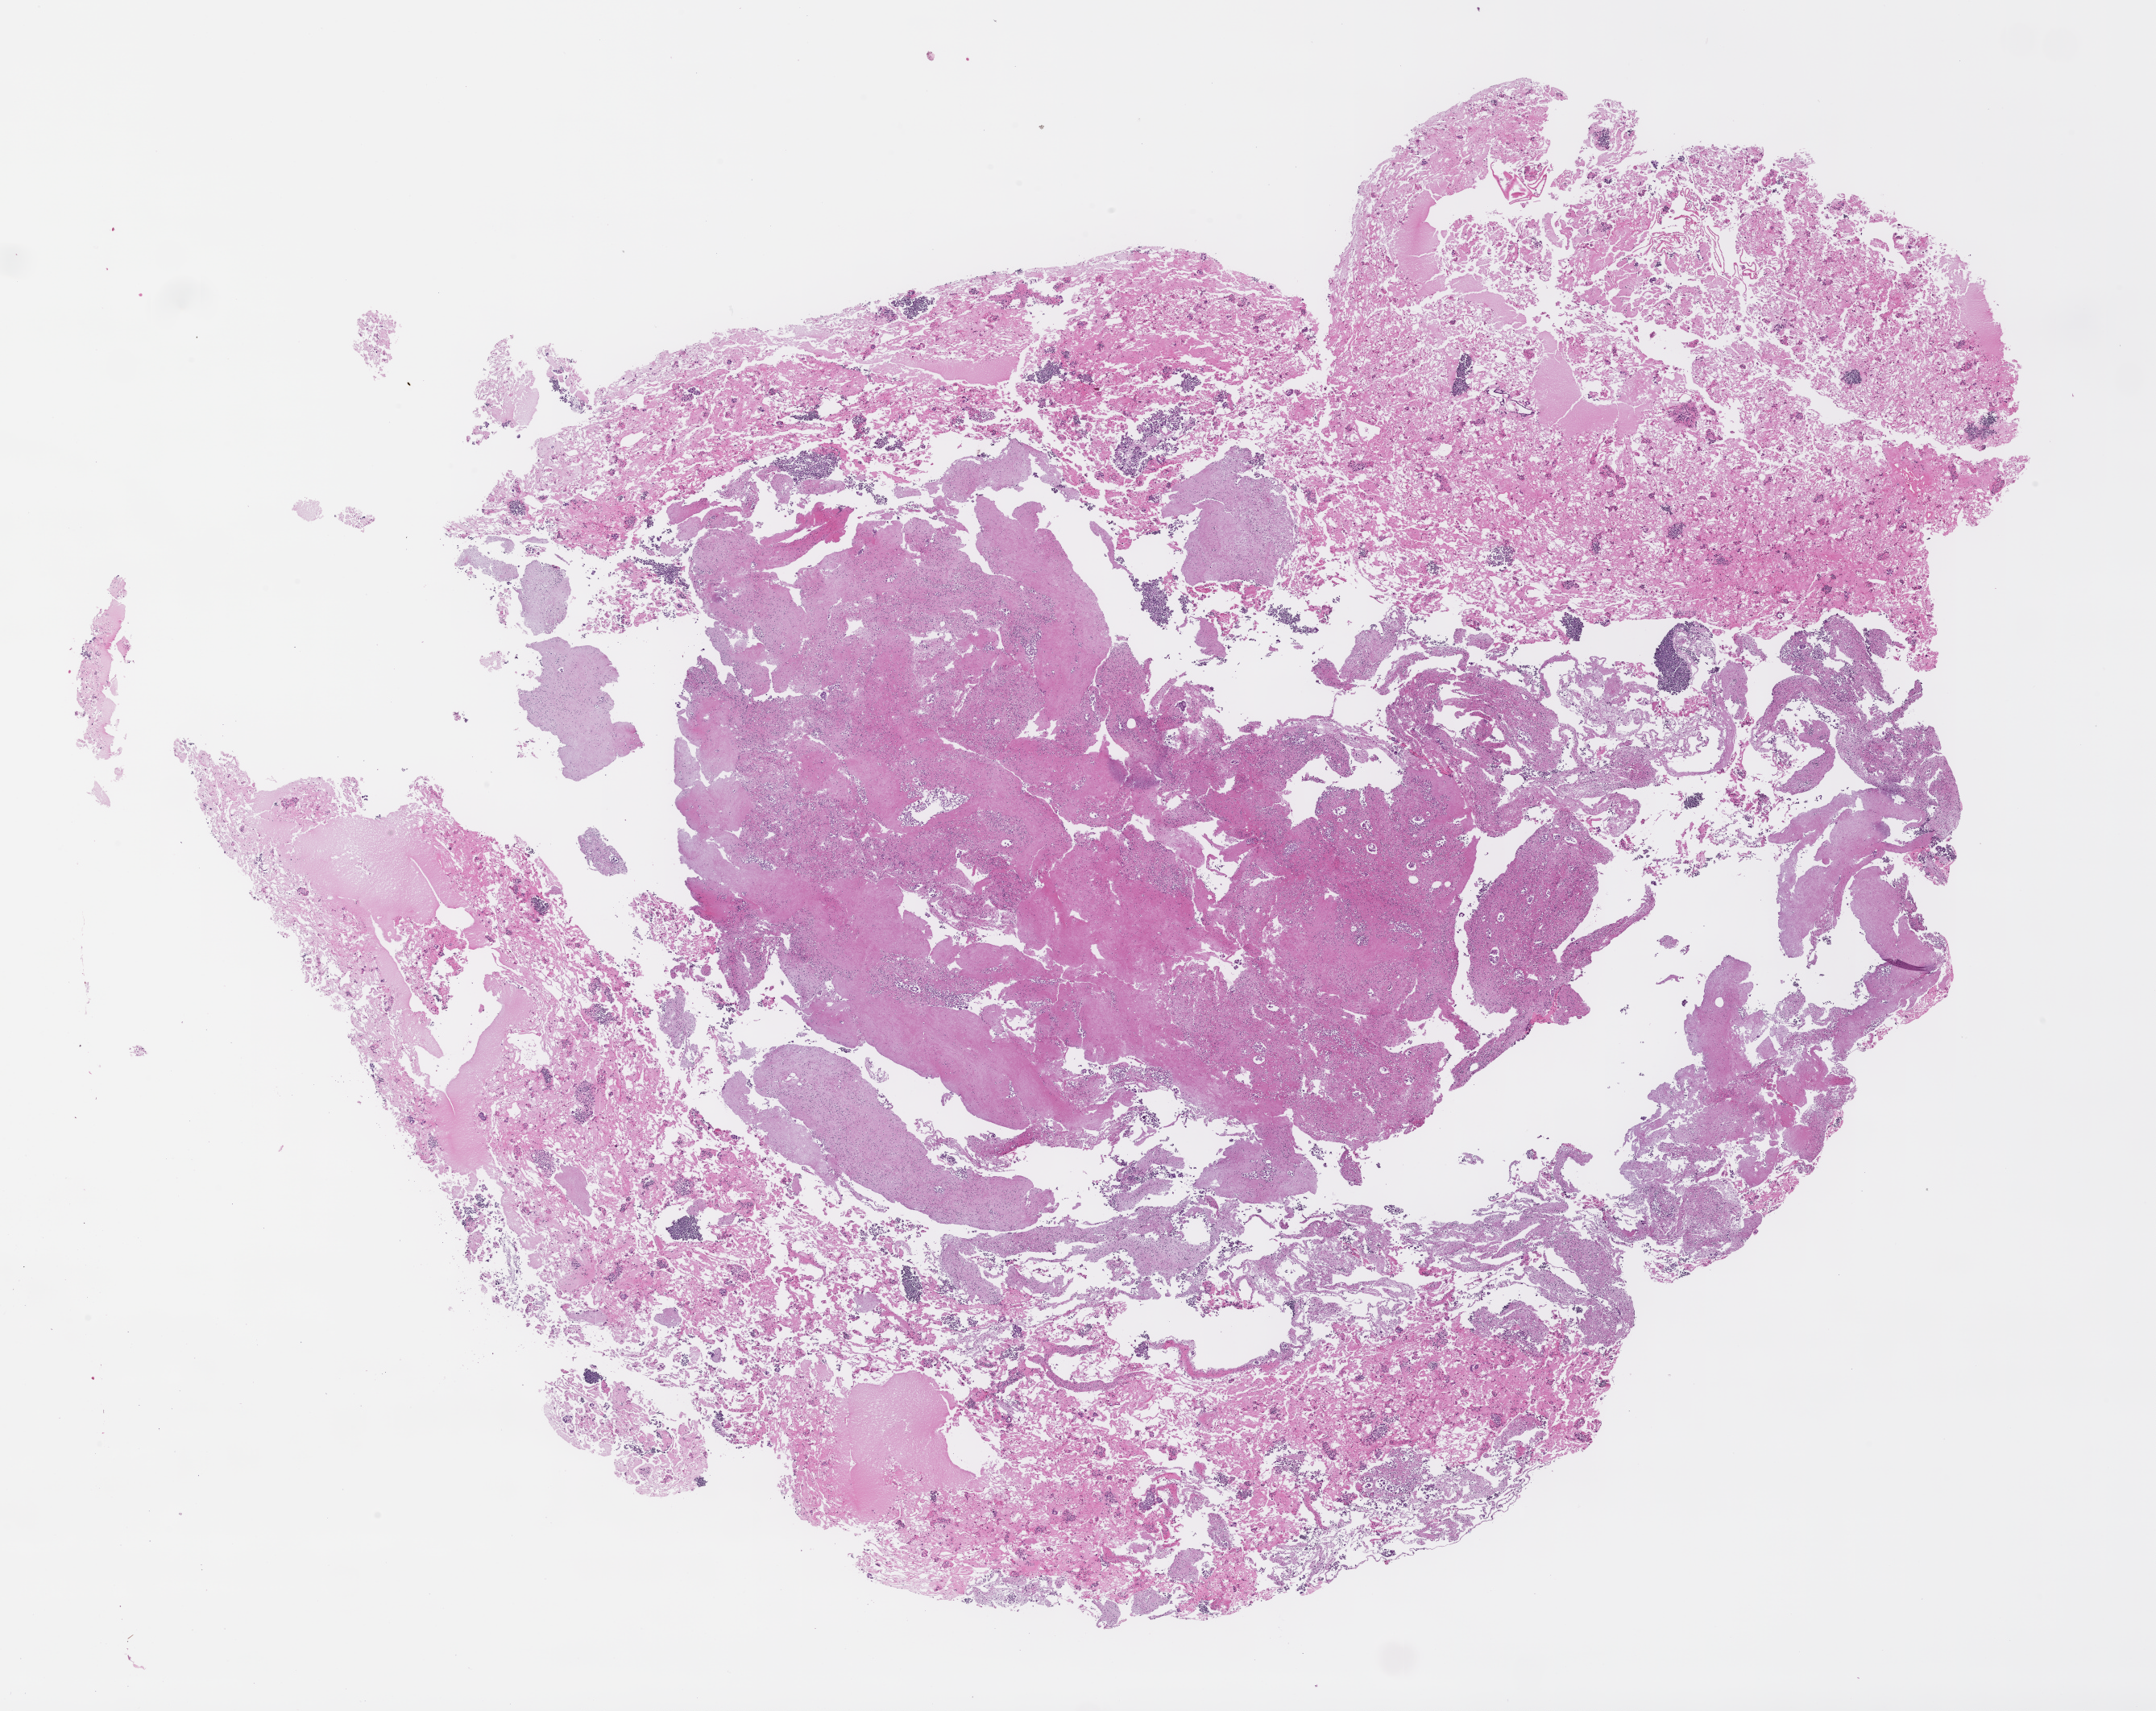
Haematoxylin and eosin whole-slide image — a low-resolution overview of the entire scanned area, about 21.6 x 17.2 mm. Formalin-fixed paraffin-embedded section. Tissue site: lung. Specimen time point: archival tissue. Patient sex: female.
This section: primary tumour tissue. Diagnosis: Non-Small Cell Lung Carcinoma.